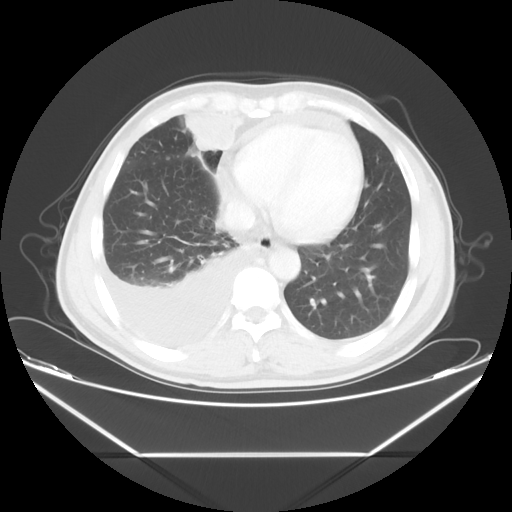
Chest CT, one axial slice; slice 17 of 56 in the series (ordered by position); lung window (W 1500 / L -600 HU); 5 mm slice thickness; 512 × 512 image matrix, field of view 412 × 412 mm. Male patient, age 57 years. Case-level facts recorded for this patient, not image findings: clinical TNM (as recorded): T2 N3 M1.
Structures marked on this image (bounding box drawn by a radiologist):
- lung tumour (recorded histology: adenocarcinoma): box from (x=181, y=106) to (x=250, y=156) px